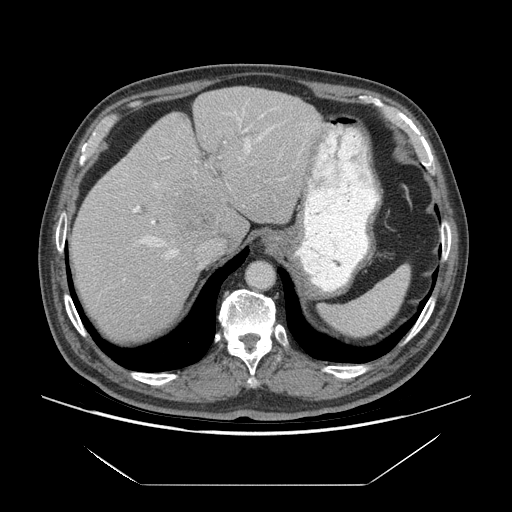
Contrast-enhanced abdominal CT (liver protocol), one axial slice; slice 52 of 75 in the series (ordered by position); soft-tissue window (W 400 / L 40 HU); 2.5 mm slice thickness; 512 × 512 image matrix, field of view 420 × 420 mm. From the clinical record (not read from this slice): diagnosis: hepatocellular carcinoma (patient treated with transarterial chemoembolisation; whether this scan precedes or follows treatment is not stated here); TNM stage (as recorded): Stage-I; Child-Pugh class: A; tumour differentiation: well differentiated; tumour nodularity: uninodular.
Structures marked on this image (semi-automatic segmentation, software-assisted and operator-edited):
- liver parenchyma outside the tumour (the mass and vessels are separate outlines, so this box may not span the whole liver): bounding box [x1, y1, x2, y2] px = [70, 86, 324, 340]
- mass: [162, 179, 226, 242]
- liver vessels: [133, 107, 308, 259]